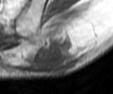
MRI of an extremity soft-tissue mass, one axial slice. Position 16 of 42 along the scan axis. MR volume resampled by the dataset authors to the PET/CT grid (not the native acquisition matrix). 3.27 mm slice thickness. 113 × 94 image matrix. Male patient. From the clinical record (not read from this slice): histological type: leiomyosarcoma; grade: intermediate; site of the primary tumour: left pelvis.
Outlined on this slice (expert contour drawn on MRI and transferred to this co-registered scan by the dataset authors):
- gross tumour volume (mass): bounding box <35,36,75,72> (left, top, right, bottom; pixels)